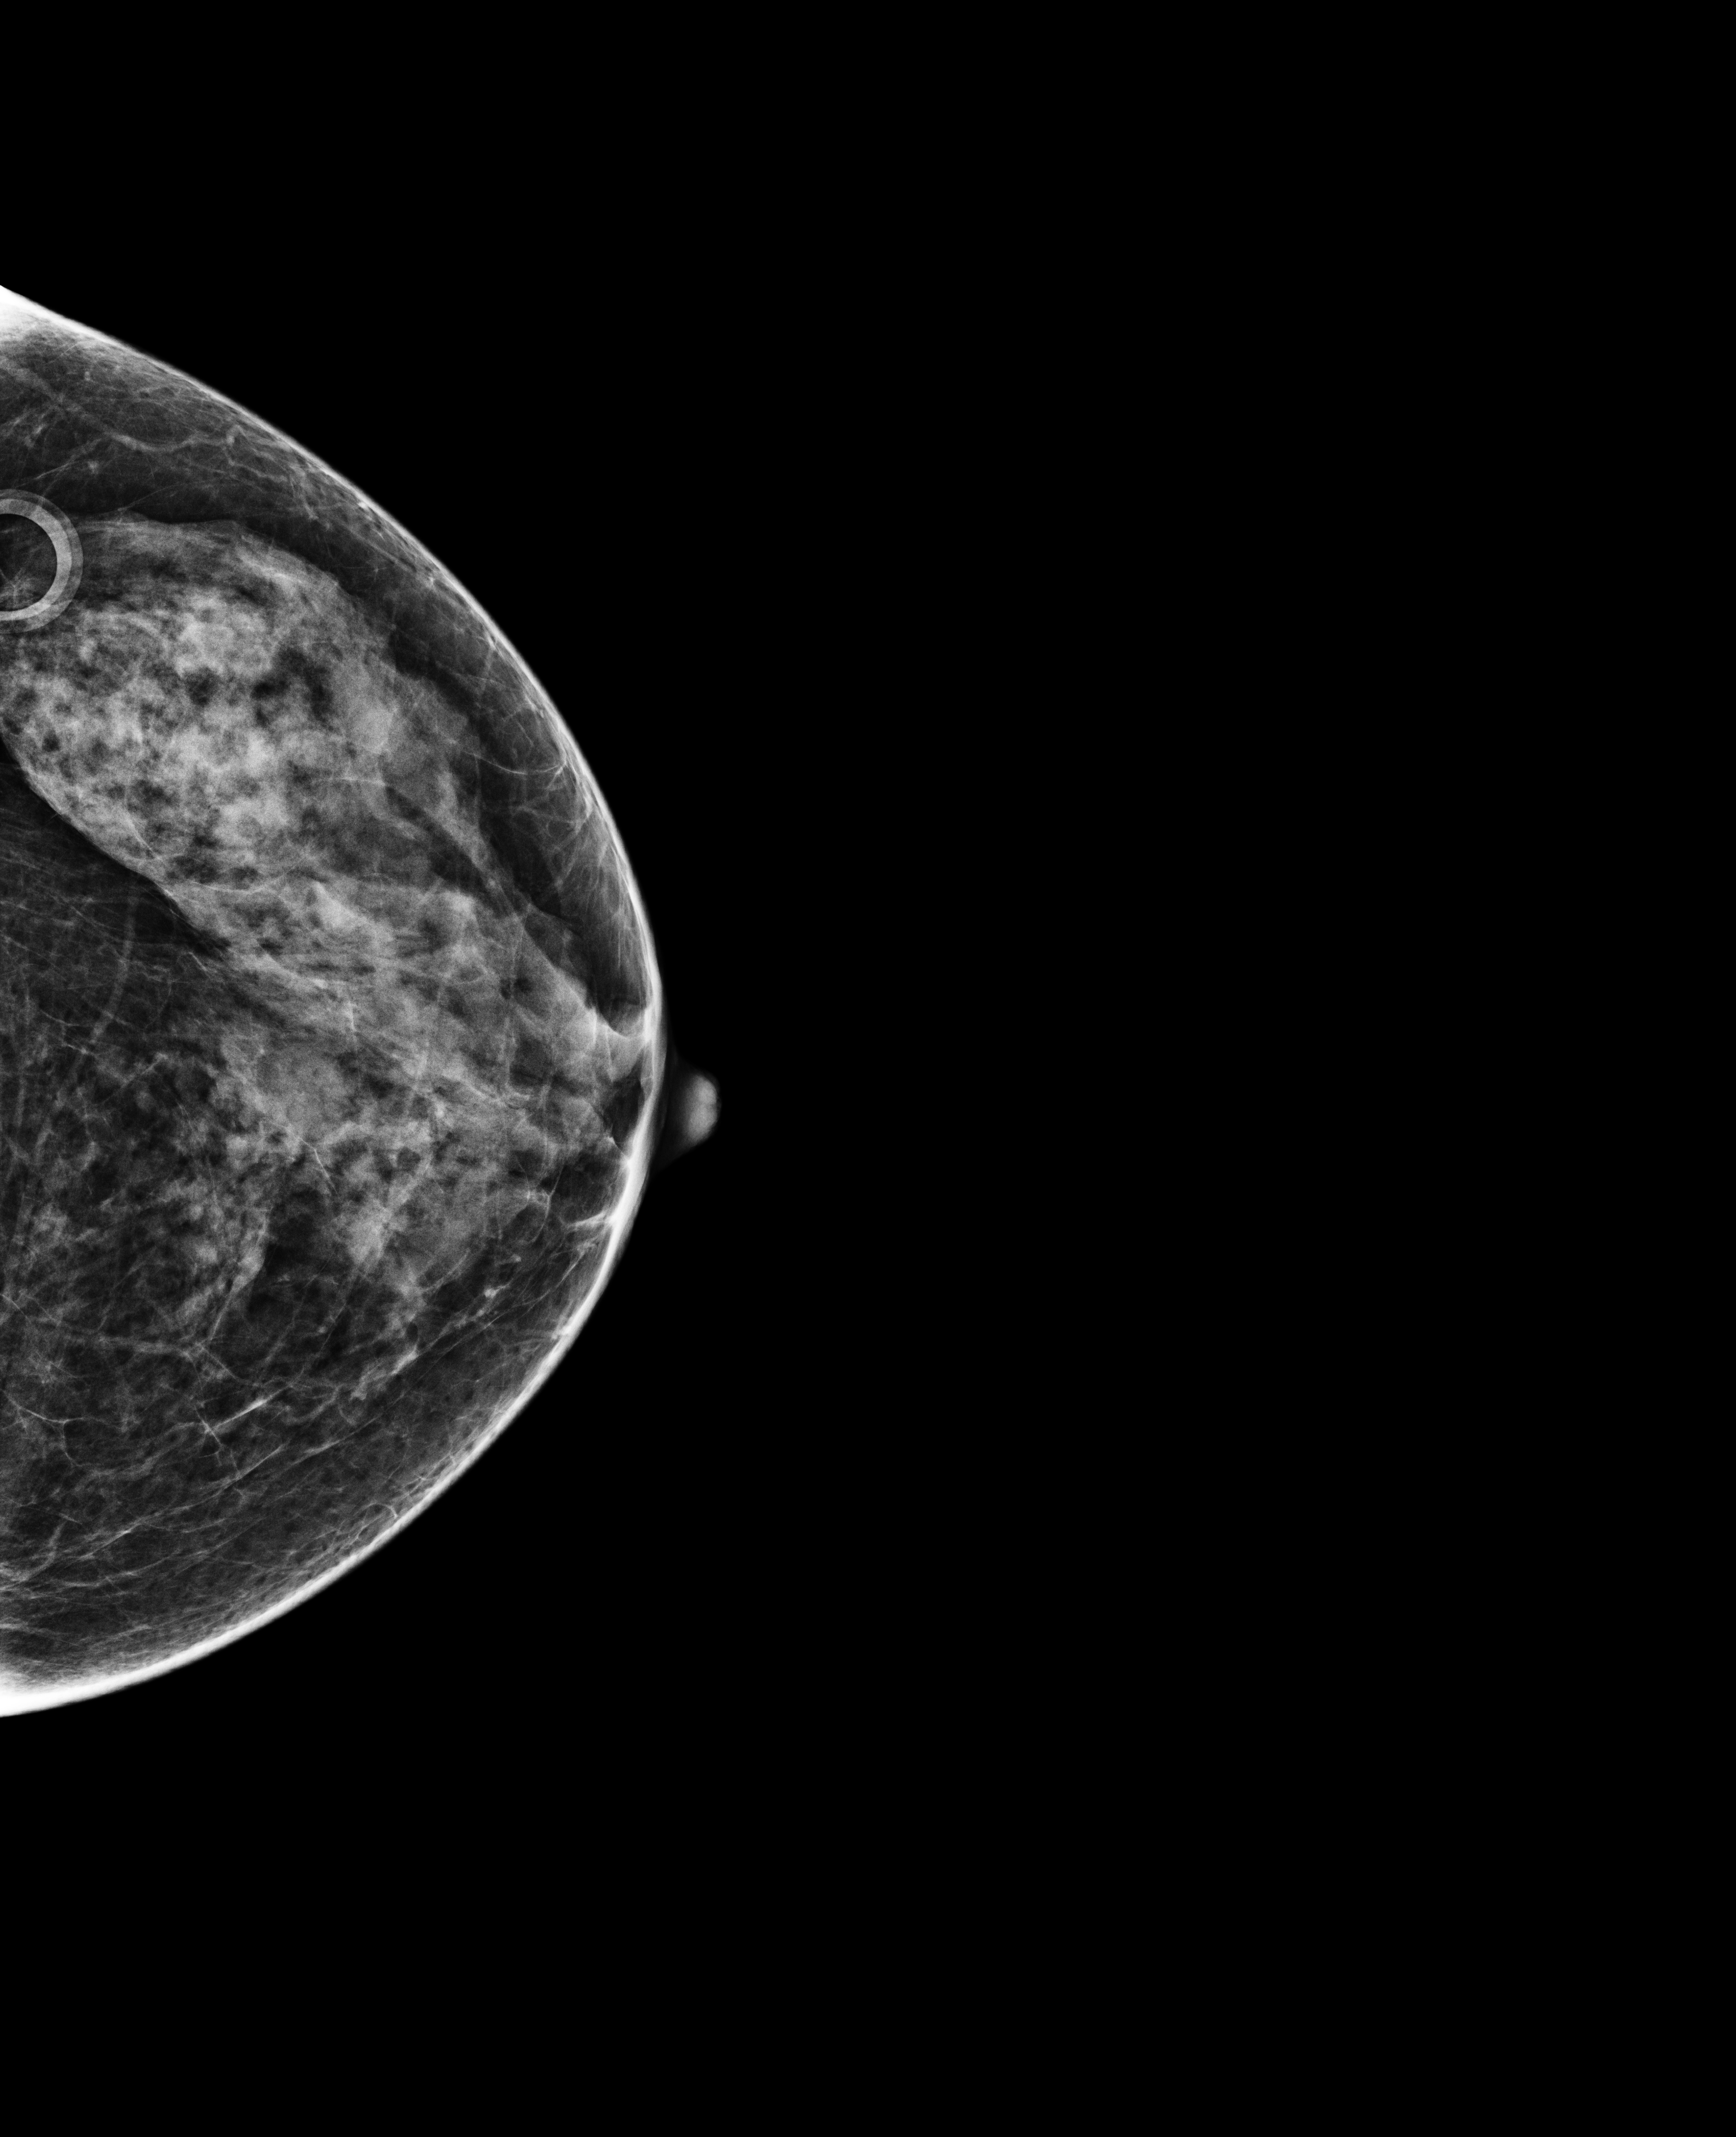
Digital mammogram (FFDM); left breast; CC view; annual screening mammography examination; system: Selenia Dimensions. Patient: female, 66 years.
- BI-RADS breast density category at the screening exam (both breasts, scale 1–4): 3
- final BI-RADS assessment for this screening round (tomosynthesis exam, both breasts): category 1
- recall: no recall after this screen